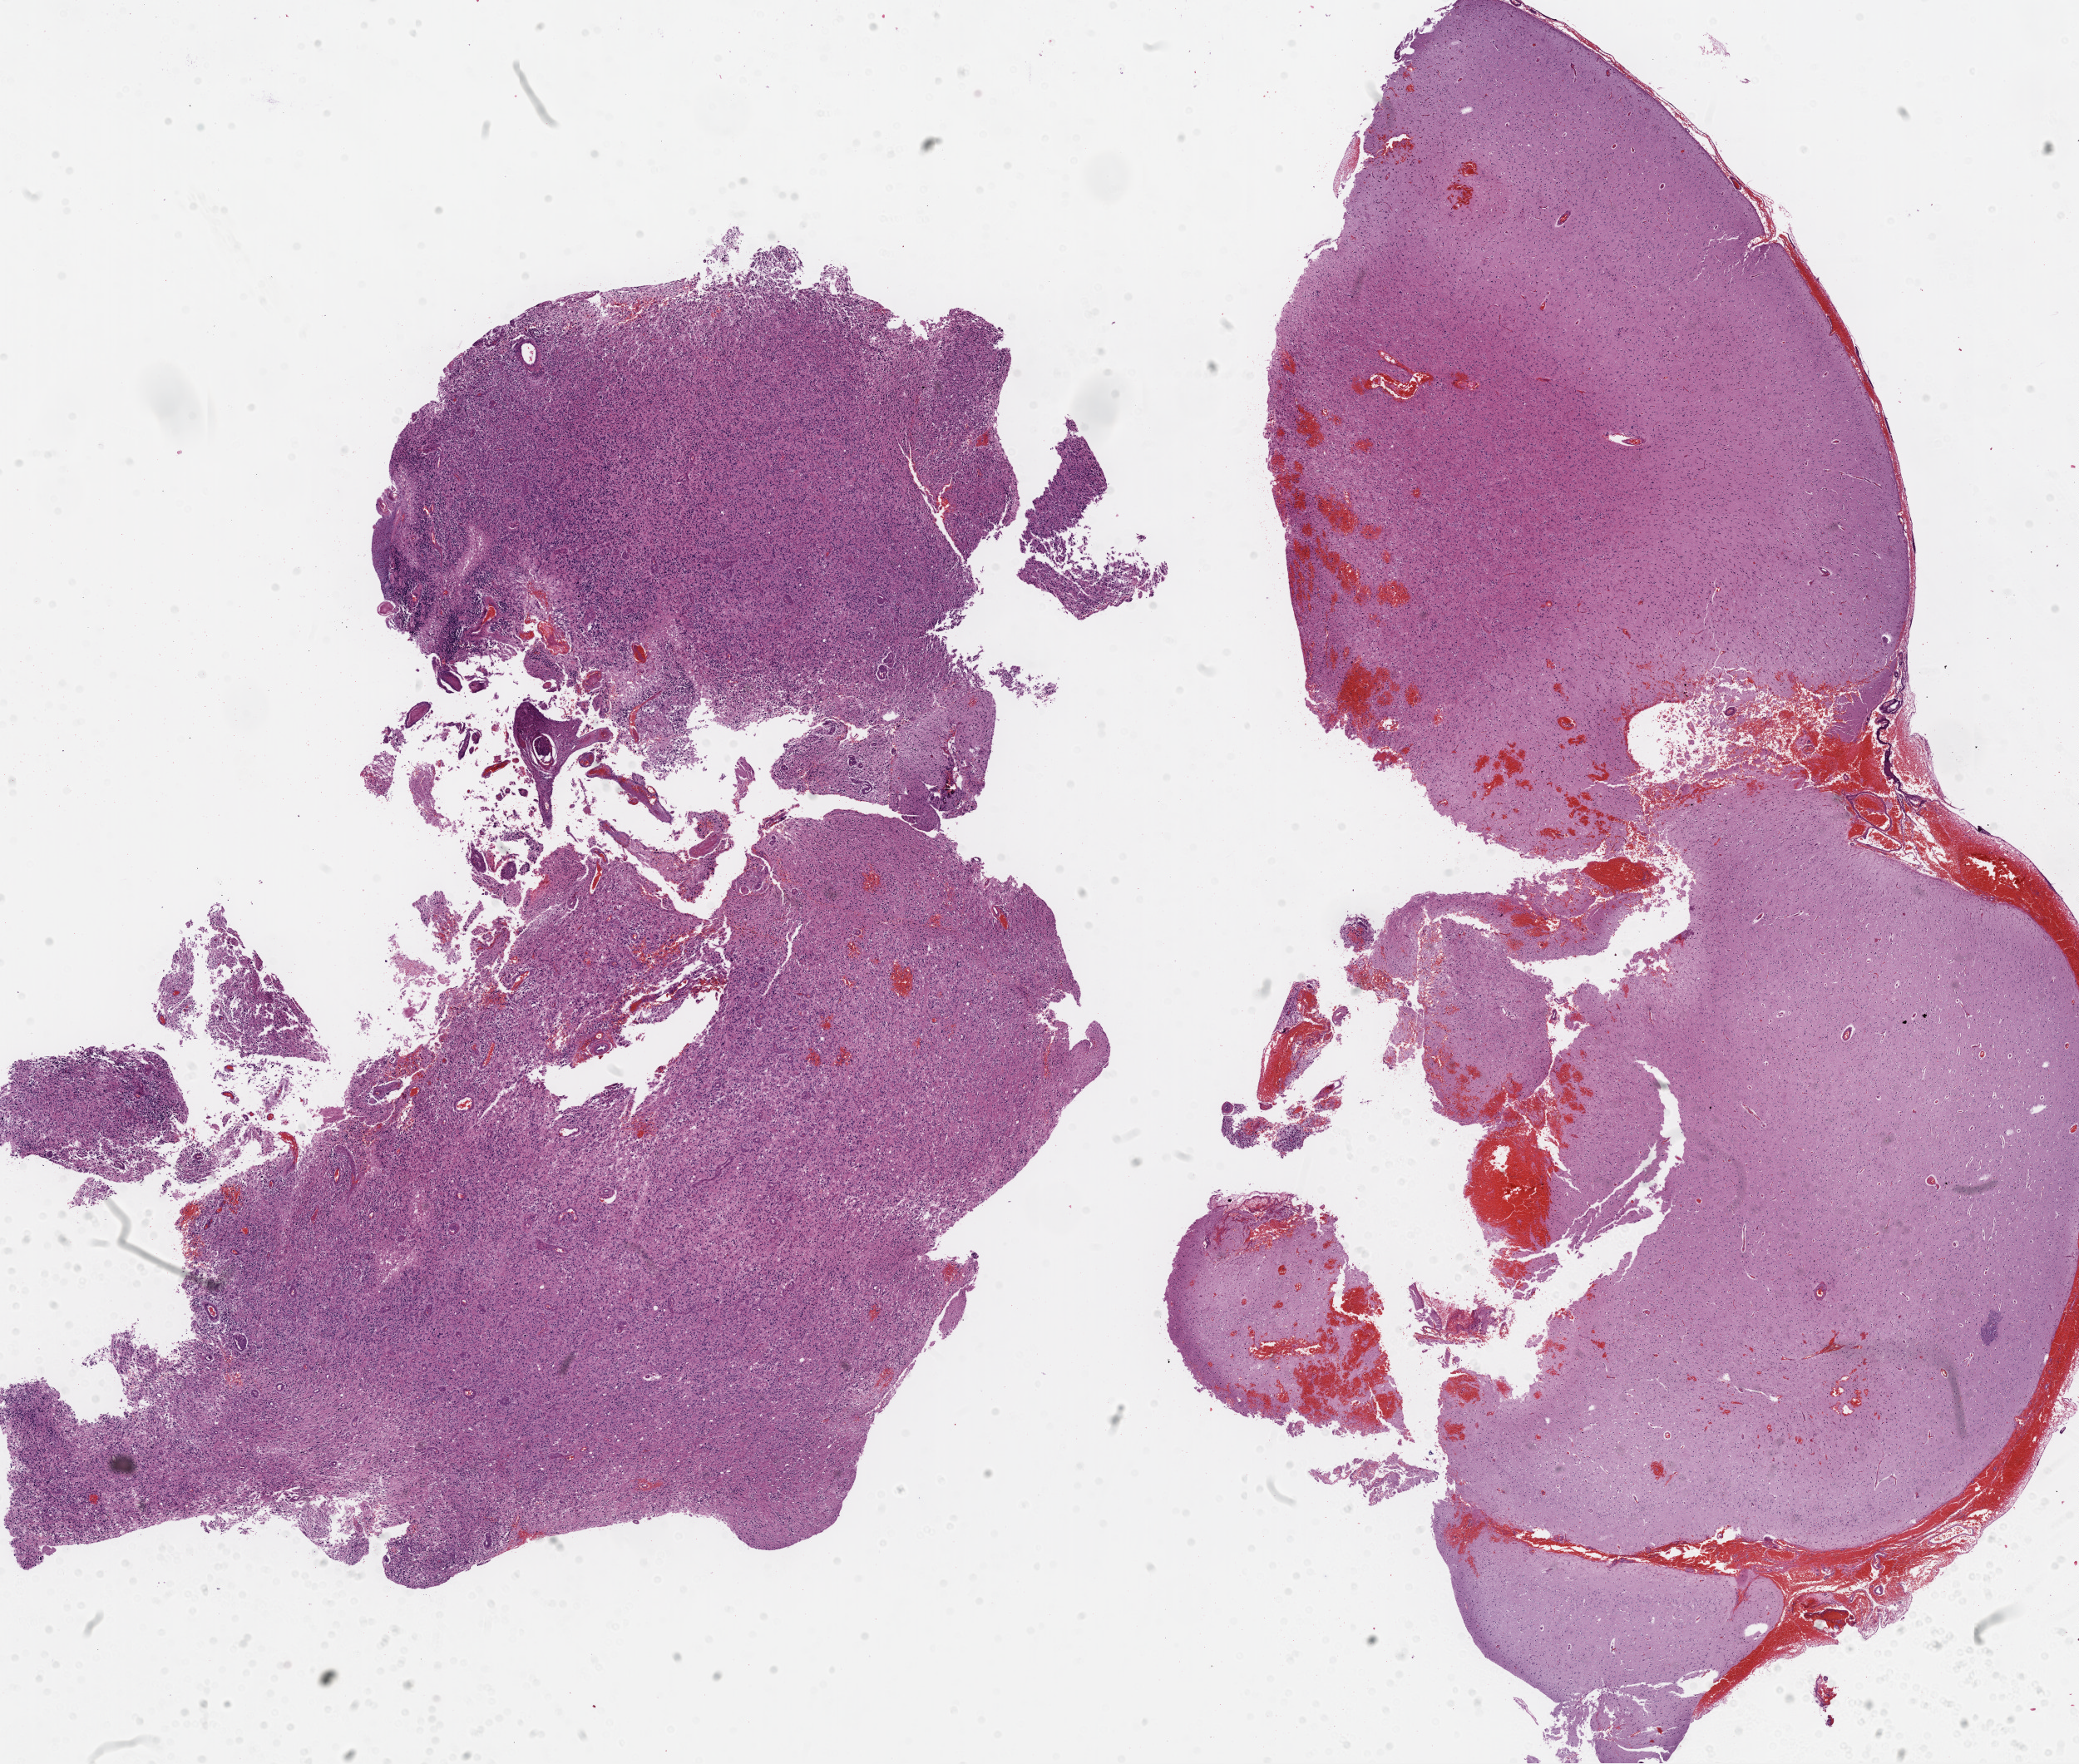
Whole-slide histology image, Hematoxylin and eosin (H&E) stained — shown as a low-resolution overview of the whole scanned area (about 20.1 x 17.0 mm, from a 20x scan); formalin-fixed paraffin-embedded (FFPE) diagnostic section; sample: primary tumour, brain. Male, age 57 years at initial diagnosis.
• histologic diagnosis: Glioblastoma